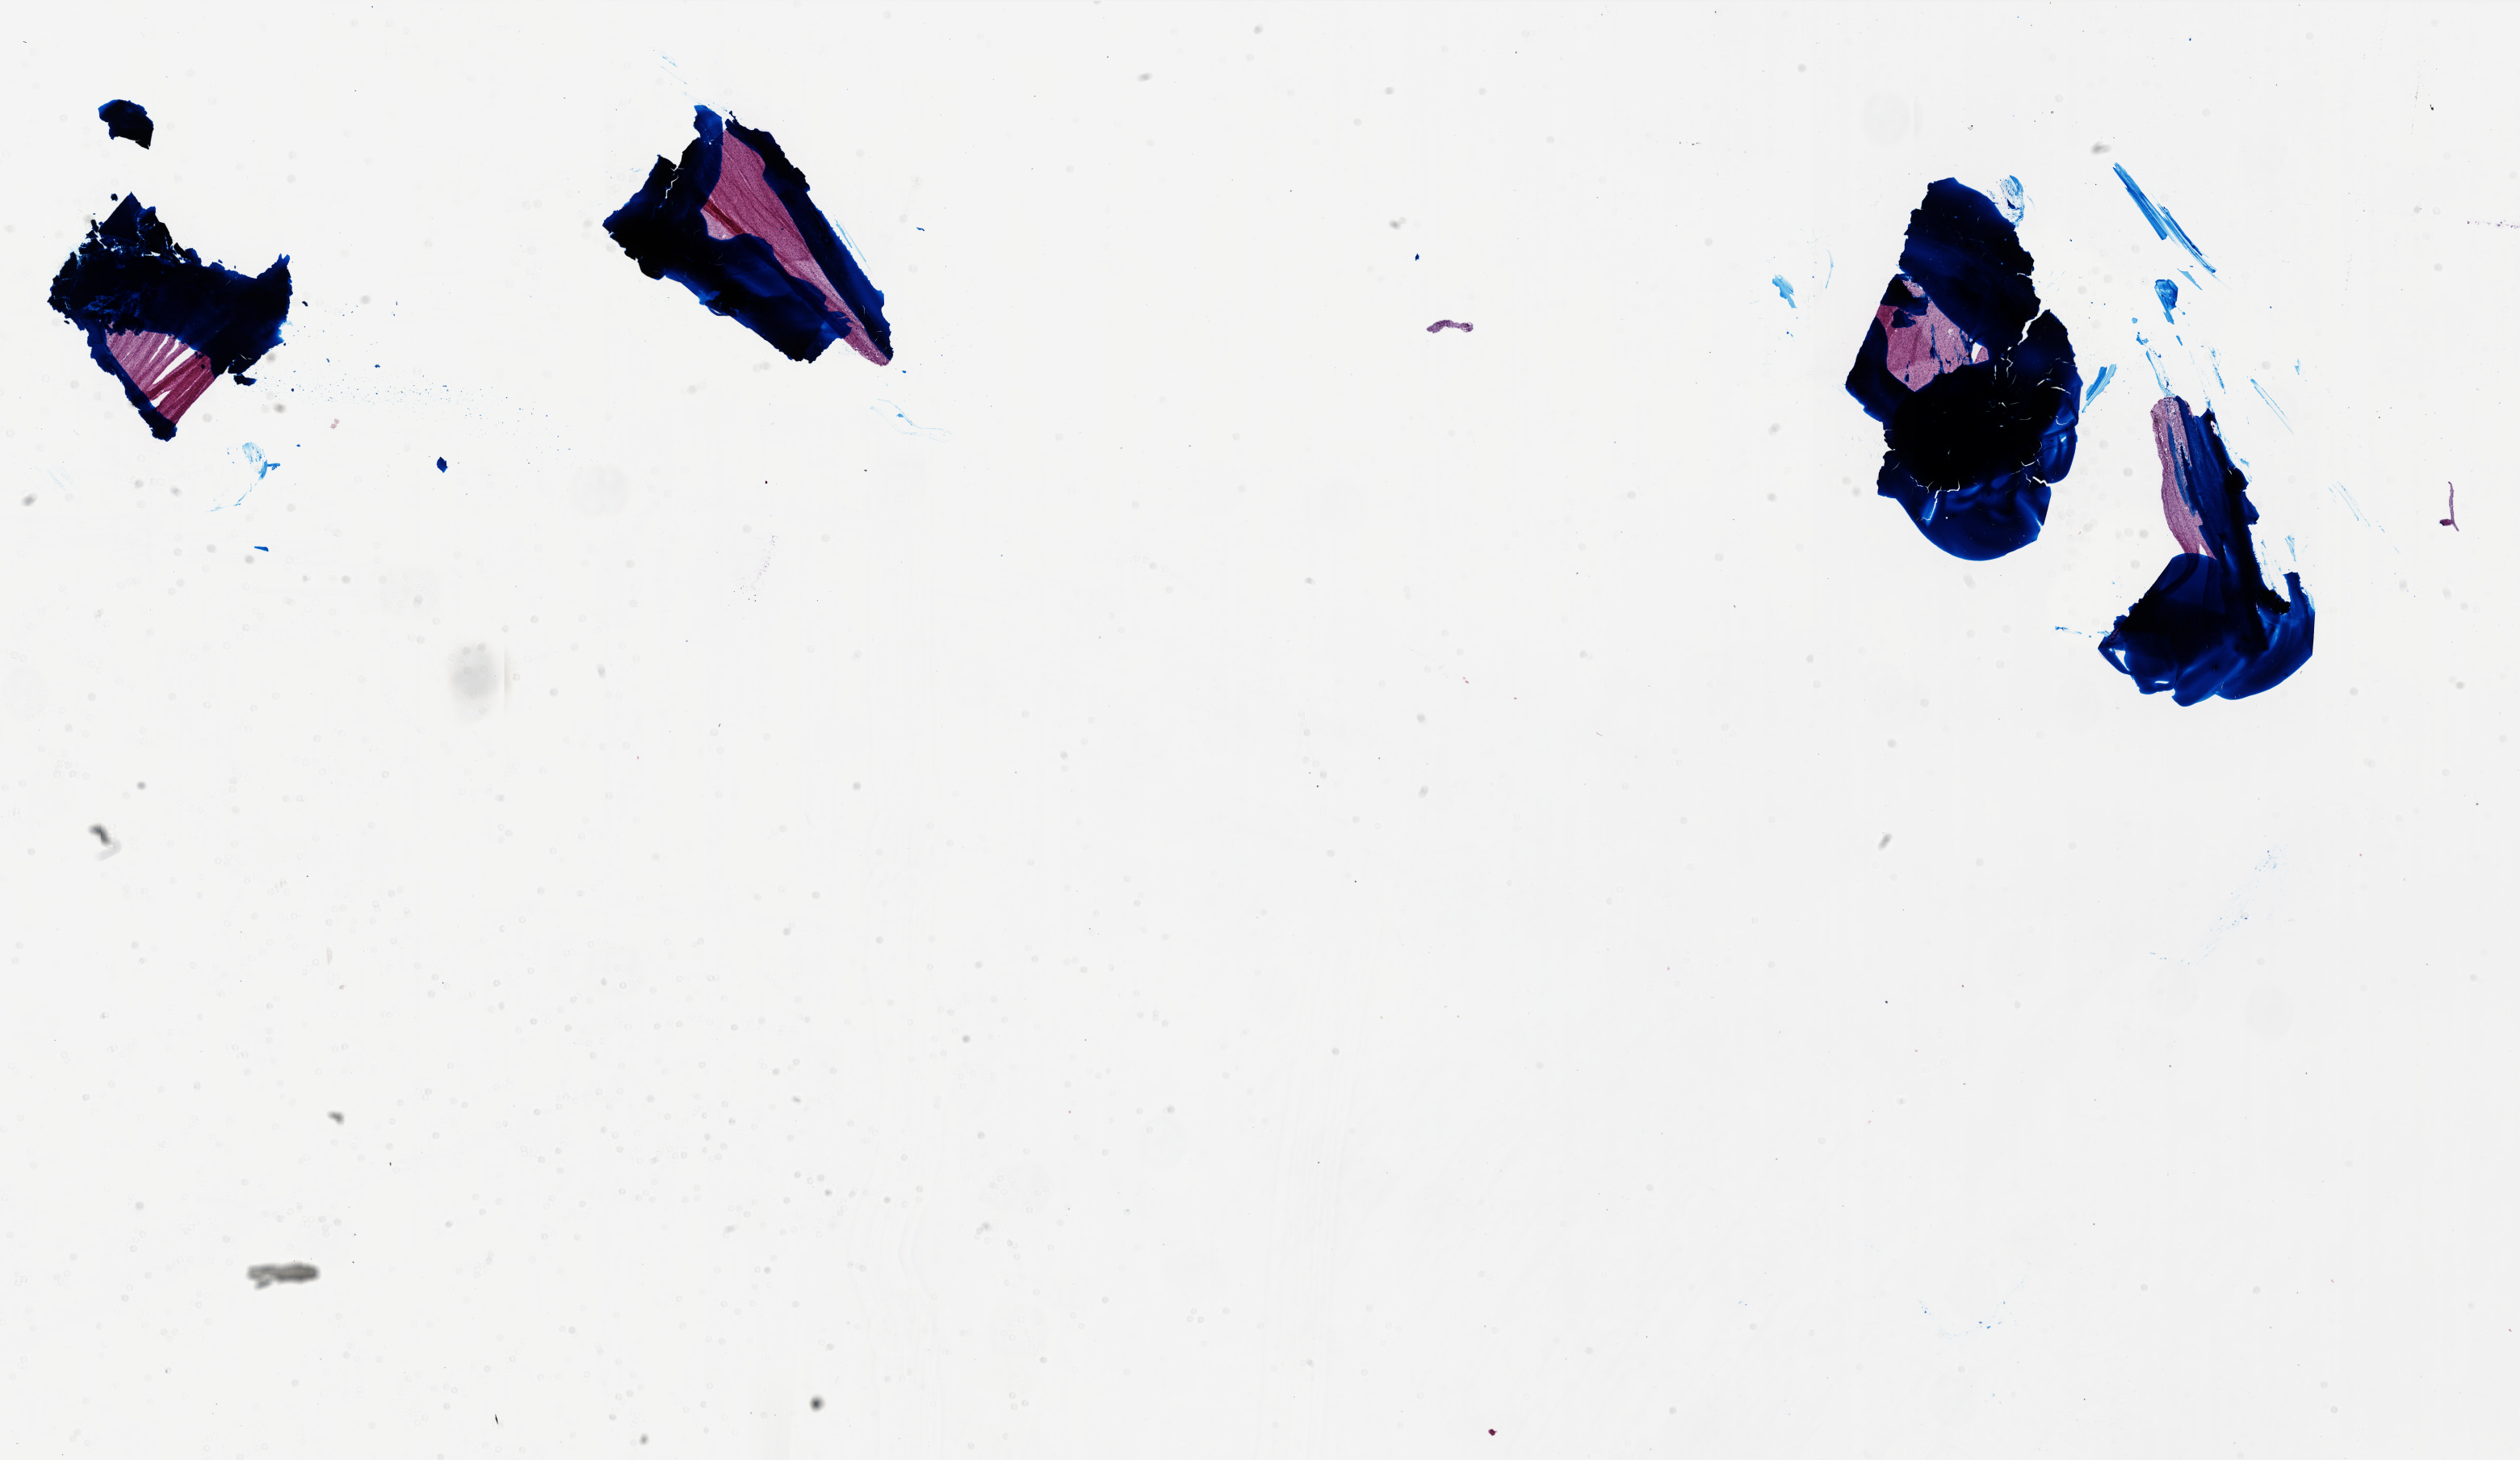
Hematoxylin and eosin (H&E) stained whole-slide image, a low-resolution overview of the entire scanned area, about 25.0 x 14.5 mm; frozen section from the top of the tissue portion; sample: primary tumour, brain. Male patient; age at initial diagnosis 47 years. Composition of this section per pathologist review: tumour cells 90%, tumour nuclei 90%, normal cells 0%, stromal cells 10%, necrosis 0%.
- diagnosis: Glioblastoma